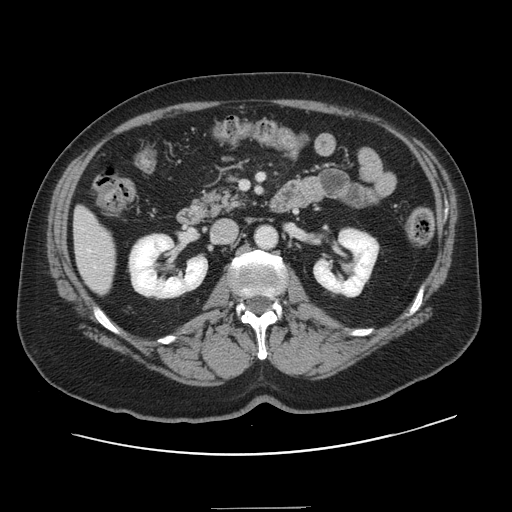
Contrast-enhanced abdominal CT, one axial slice. 120 kVp. Intravenous contrast given. Soft-tissue window (W 400 / L 40 HU). 2.5 mm slice thickness. 512 × 512 image matrix, field of view 402 × 402 mm. Male patient, age 62 years. Case-level facts recorded for this patient, not image findings: diagnosis: colorectal cancer liver metastases, imaged before liver resection; multiple liver metastases: yes; largest metastasis: 2.7 cm; disease in both lobes: no.
Structures marked on this image (expert manual segmentation):
- liver: bounding box [x1, y1, x2, y2] px = [74, 209, 115, 293]